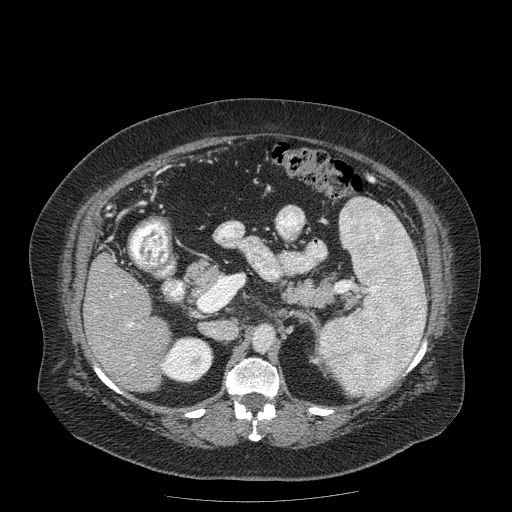
Contrast-enhanced abdominal CT (liver protocol), one axial slice; slice 83 of 204 in the series (ordered by position); 120 kVp; soft-tissue window (W 400 / L 40 HU); 2.5 mm slice thickness; 512 × 512 image matrix, field of view 440 × 440 mm. From the clinical record (not read from this slice): diagnosis: hepatocellular carcinoma (patient treated with transarterial chemoembolisation; whether this scan precedes or follows treatment is not stated here); TNM stage (as recorded): Stage-IIIB; Child-Pugh class: A.
Annotated regions visible in this slice (semi-automatic segmentation, software-assisted and operator-edited):
- liver parenchyma outside the tumour (the mass and vessels are separate outlines, so this box may not span the whole liver): box from (x=84, y=254) to (x=170, y=392) px
- liver vessels: (x=96, y=295)–(x=134, y=366)